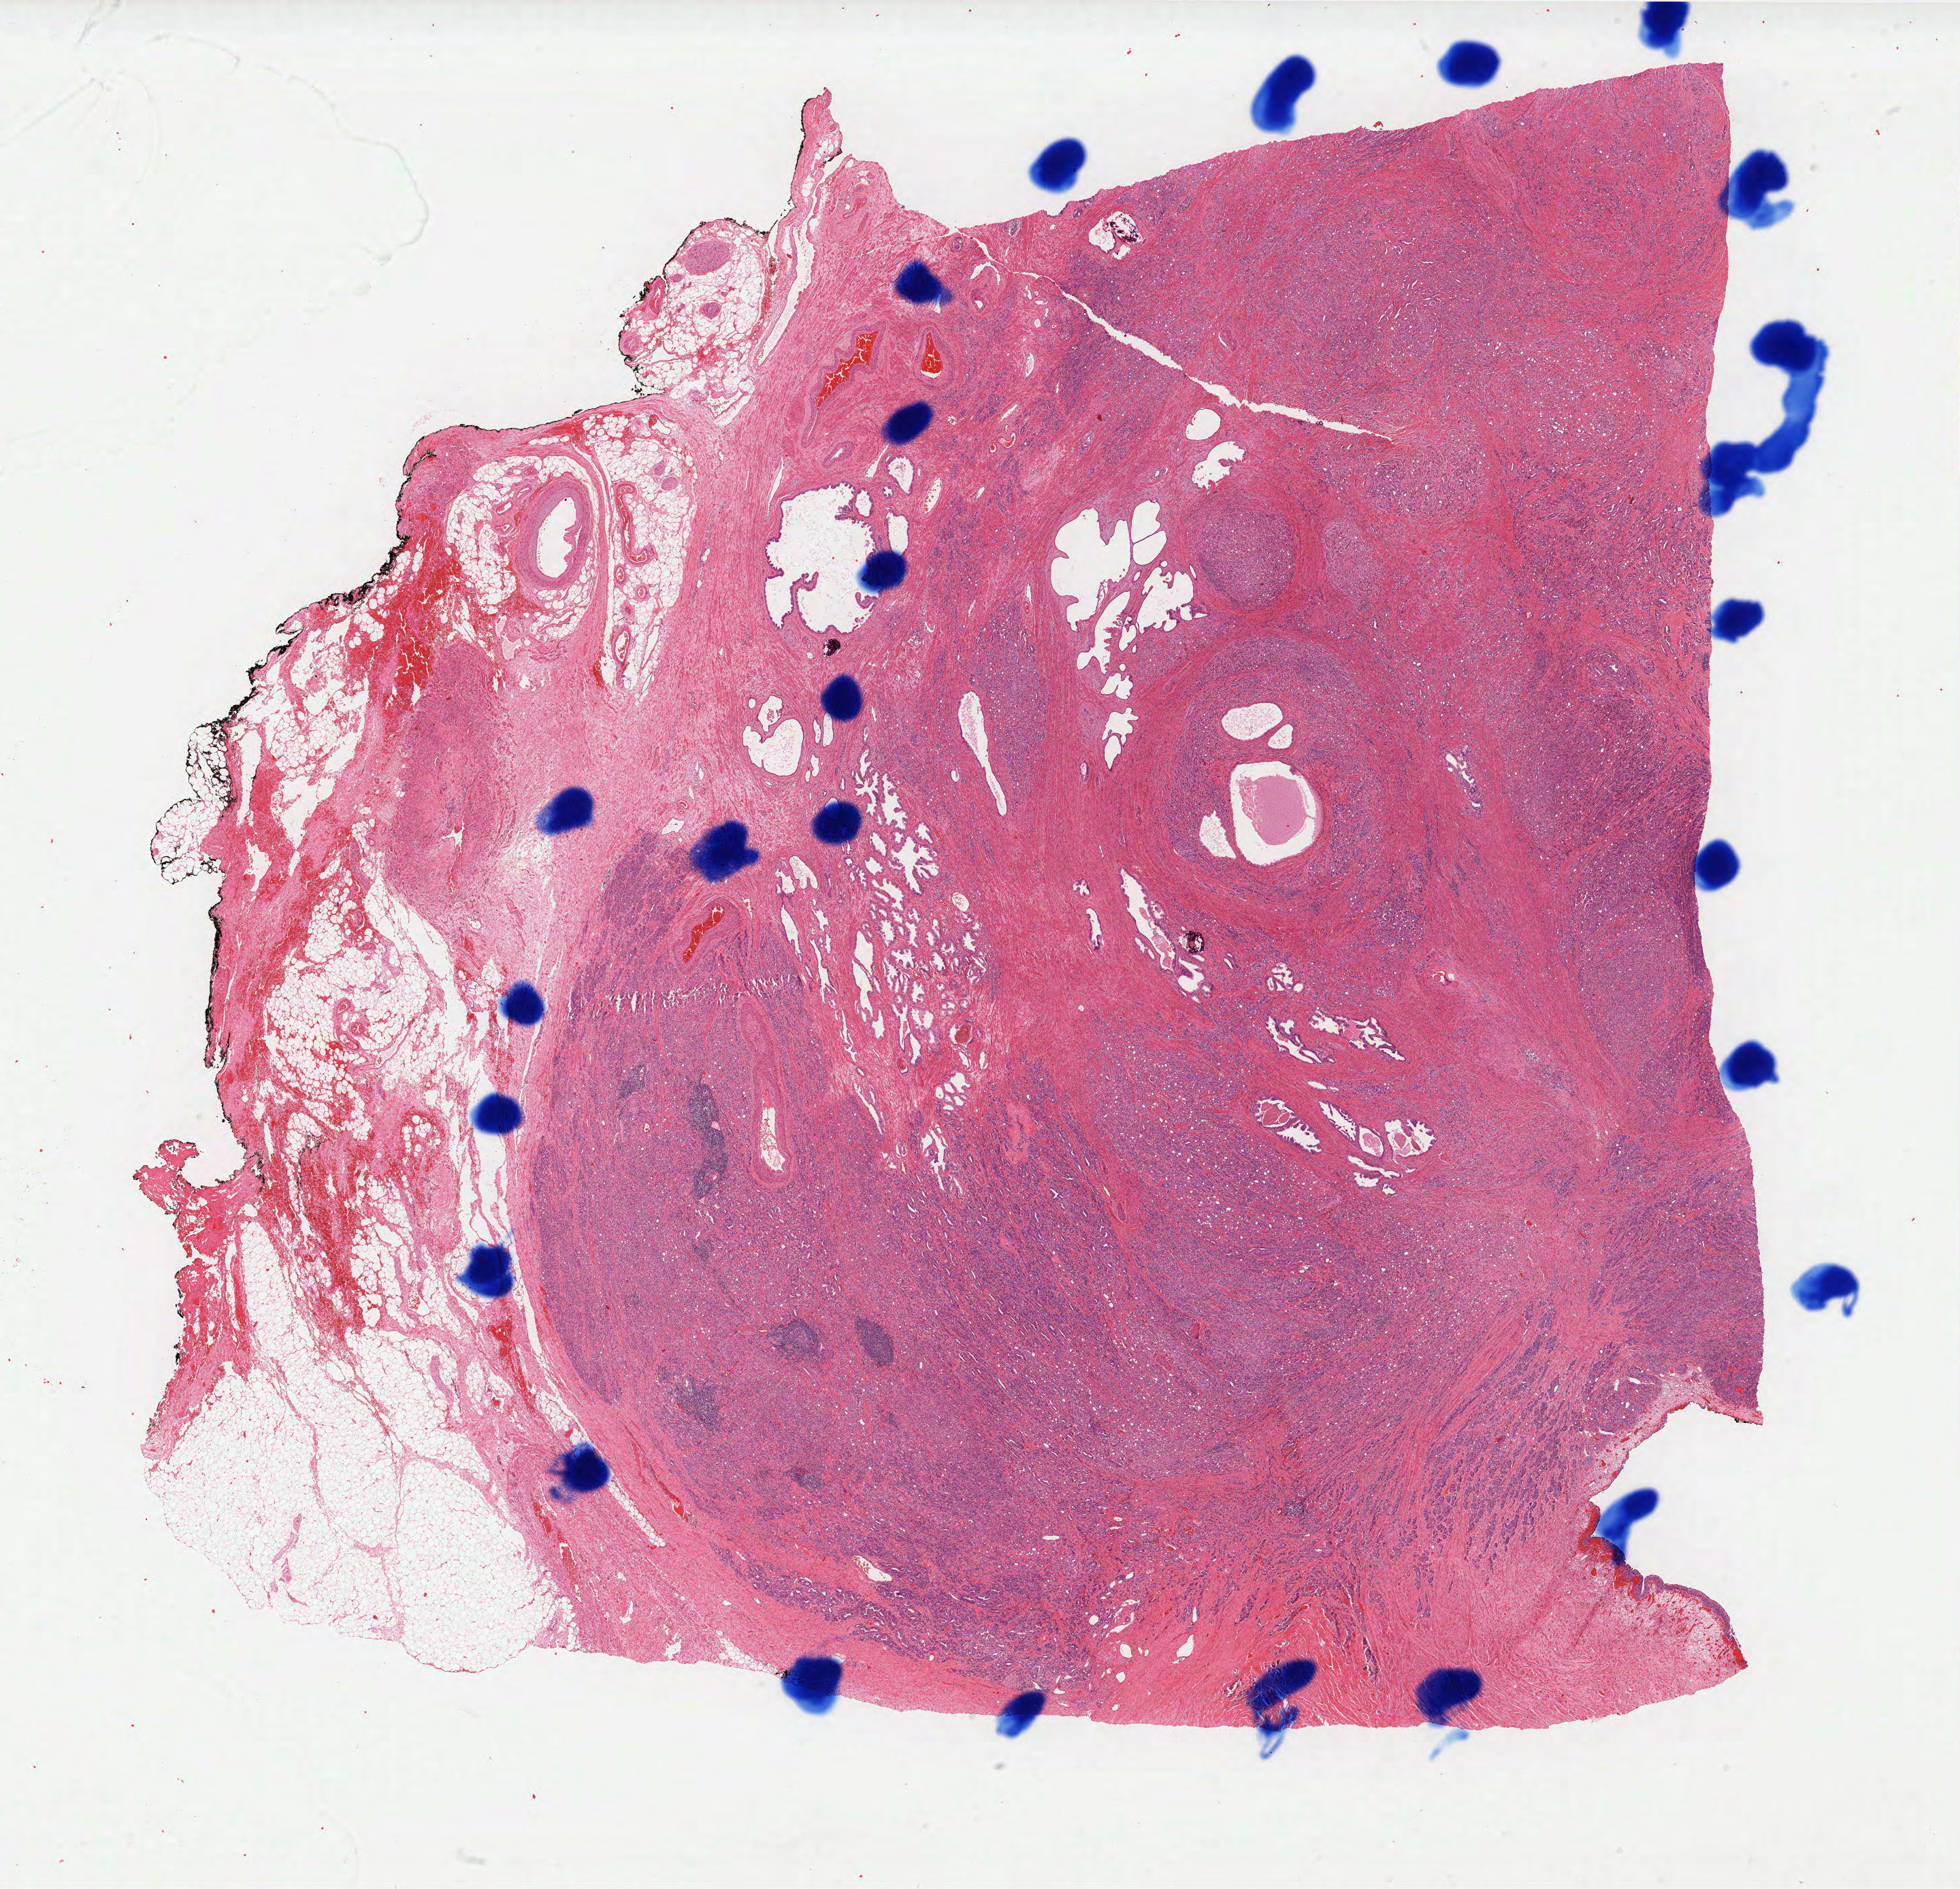
Whole-slide histology image, H&E — low-resolution overview of the scanned area, about 23.0 x 22.2 mm, formalin-fixed paraffin-embedded (FFPE) diagnostic section, prostate, primary tumour sample. Male patient; age at initial diagnosis 76 years. Gleason score: 9 (4+5).
Pathologic diagnosis: Adenocarcinoma, NOS (prostate gland). Laterality: bilateral.